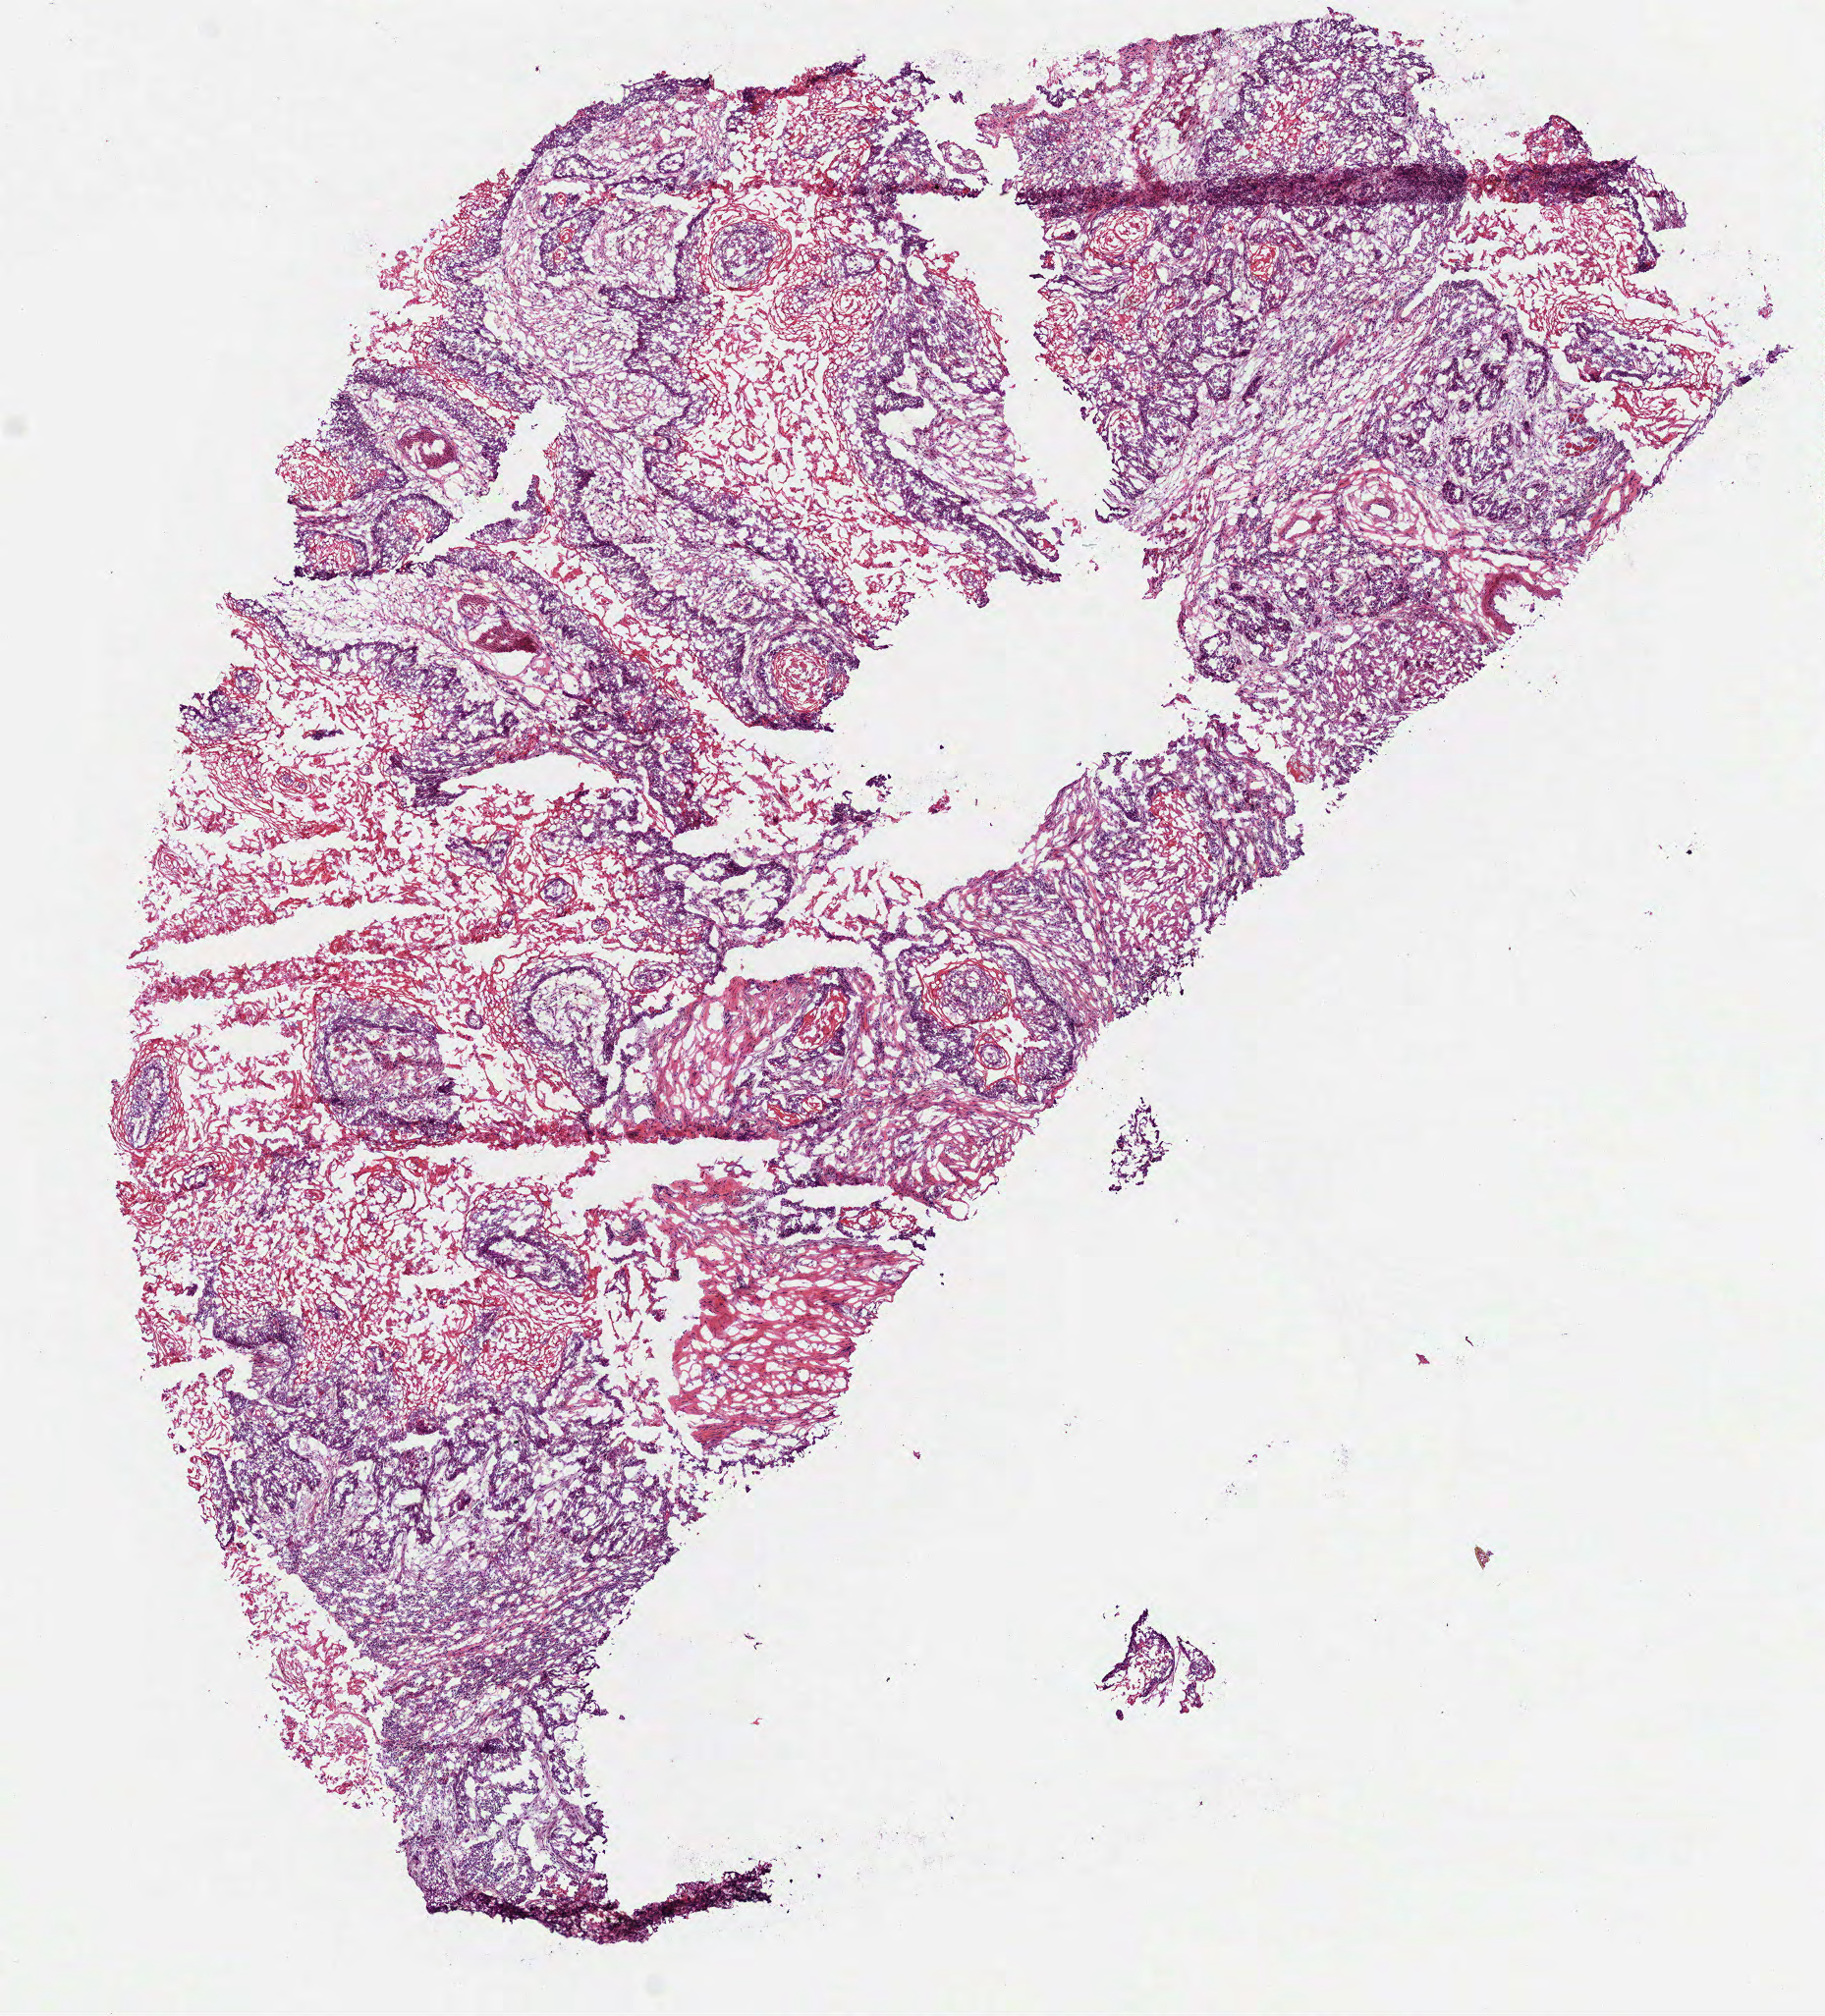
Hematoxylin and eosin (H&E) stained whole-slide image, a low-resolution overview of the entire scanned area, about 7.5 x 8.3 mm. Frozen section from the top of the tissue portion. Head and neck, primary tumour sample. Male, age 64 years at initial diagnosis. Histologic grade: G1 (well differentiated). Pathologist review of this section (percent, as recorded): tumour cells 85%, tumour nuclei 70%, normal cells 0%, stromal cells 15%, necrosis 0%.
• histologic diagnosis: Squamous cell carcinoma, NOS (overlapping lesion of lip, oral cavity and pharynx)
• AJCC pathologic stage: II